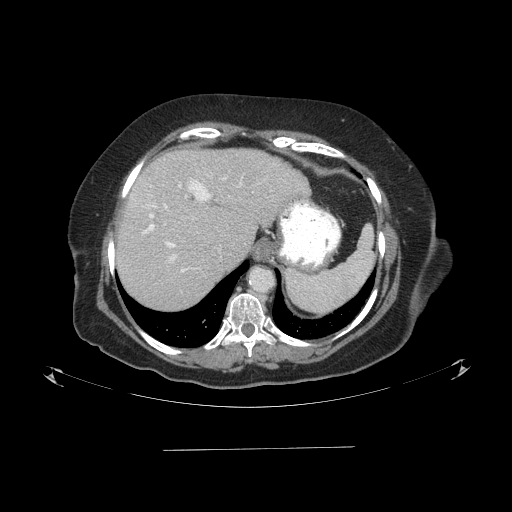
Contrast-enhanced abdominal CT (liver protocol), one axial slice; position 69 of 103 along the scan axis; reconstruction kernel STANDARD; 120 kVp; one of 2 acquisitions stored at this slice position; soft-tissue window (W 400 / L 40 HU); 2.5 mm slice thickness; 512 × 512 image matrix, field of view 500 × 500 mm. Case-level facts recorded for this patient, not image findings: diagnosis: hepatocellular carcinoma (patient treated with transarterial chemoembolisation; whether this scan precedes or follows treatment is not stated here); TNM stage (as recorded): Stage-IIIA; Child-Pugh class: A; tumour differentiation: poorly differentiated; tumour size: 5.2 cm.
Annotated regions visible in this slice (semi-automatically segmented with operator editing):
- liver parenchyma outside the tumour (the mass and vessels are separate outlines, so this box may not span the whole liver): box from (x=116, y=148) to (x=310, y=310) px
- liver vessels: (x=142, y=178)–(x=242, y=273)